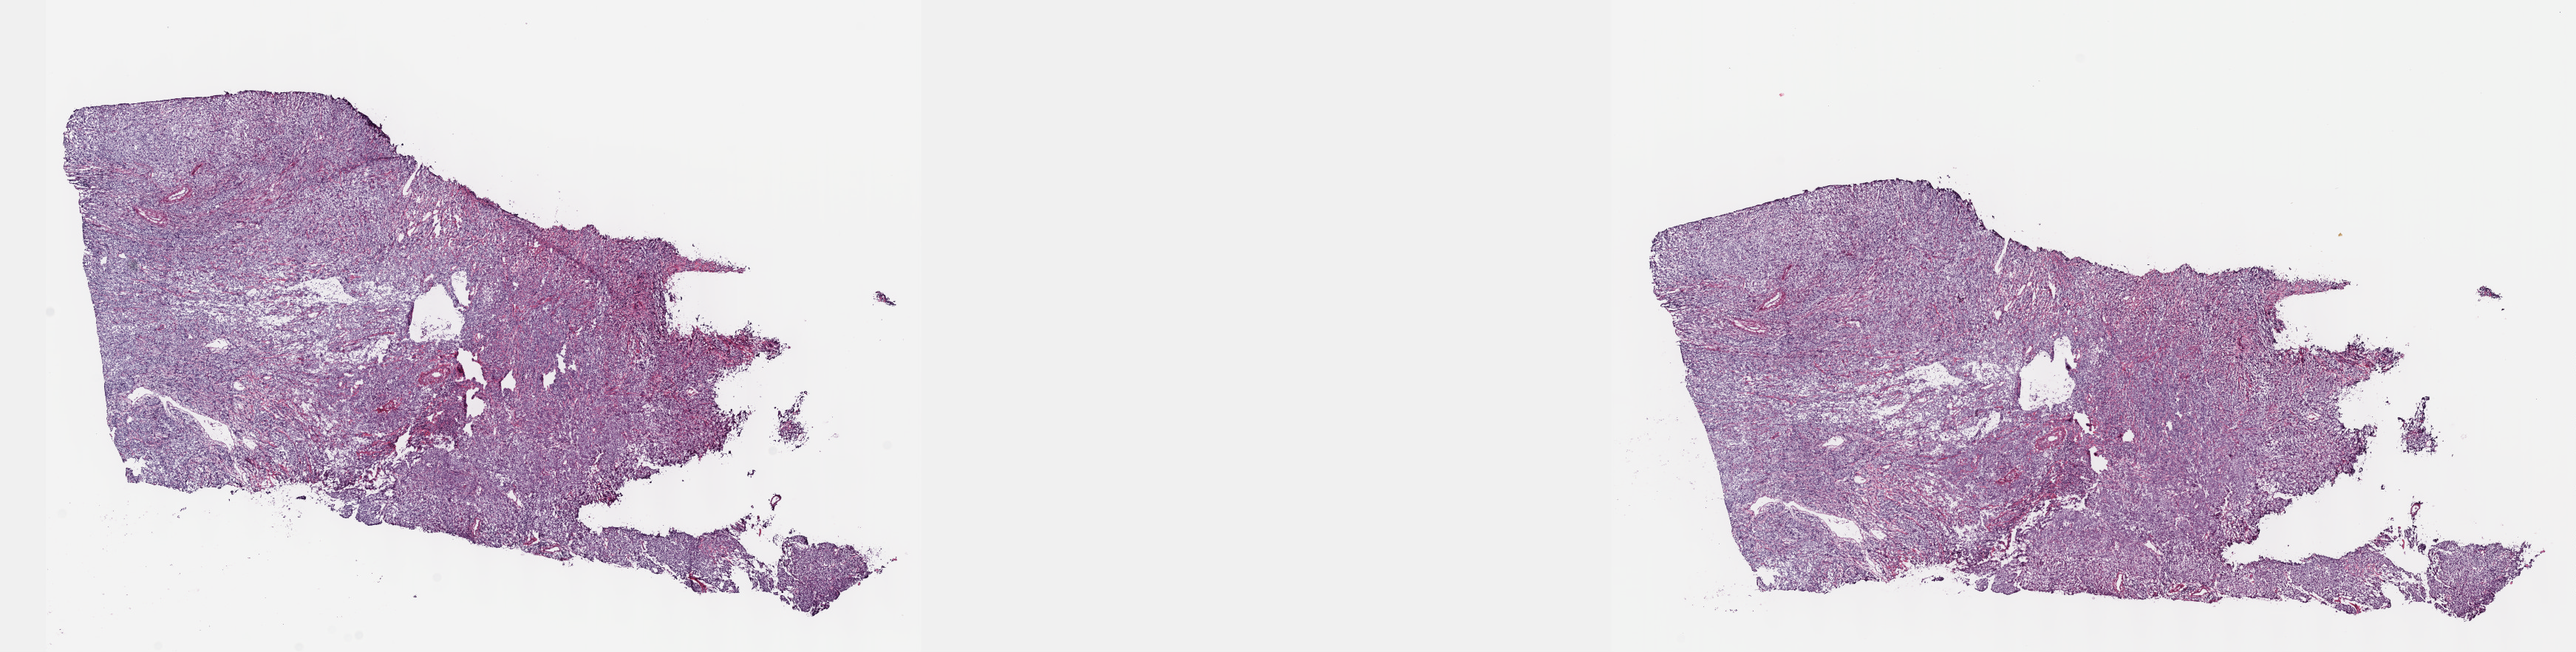
Digitized Hematoxylin and eosin (H&E) stained tissue section (whole slide) — whole scanned area (about 28.2 x 7.1 mm) shown as a low-resolution overview. Frozen section from the top of the tissue portion. Sample: primary tumour, cervix. Female, age 43 years at initial diagnosis. Histologic grade: G2 (moderately differentiated). Slide review estimates, as recorded: tumour cells 80%, tumour nuclei 80%, normal cells 0%, stromal cells 10%, necrosis 10%. Inflammatory infiltration, as recorded: lymphocyte infiltration 40%, monocyte infiltration 20%, neutrophil infiltration 20%.
FIGO stage: IIA2. Histologic diagnosis: Squamous cell carcinoma, large cell, nonkeratinizing, NOS (cervix uteri).